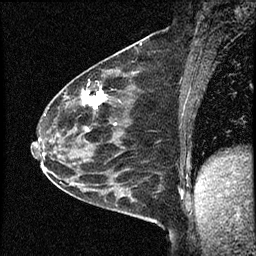
Breast MRI (dynamic contrast-enhanced), one sagittal slice. Slice 34 of 60 in the series (ordered by position). Dynamic contrast-enhanced study with each time point stored as its own series, time point 2 of 4 at this slice position (early post-contrast, ordered by acquisition time). 1.5 T. TE 4.2 ms, TR 17.6 ms. 2 mm slice thickness. 256 × 256 image matrix. Patient: female, 53 years. From the clinical record (not read from this slice): setting: breast cancer imaged before/during neoadjuvant chemotherapy; receptor status: HR-positive, HER2-negative.
Annotated regions visible in this slice (semi-automatic segmentation, software-assisted and operator-edited):
- analysis volume of interest (the breast-tissue region the enhancement analysis was run in; not a lesion): bounding box [x1, y1, x2, y2] px = [42, 69, 149, 199]
- tumour enhancement mask (voxels above the 100 % enhancement threshold inside the analysis volume of interest): [82, 90, 106, 132]